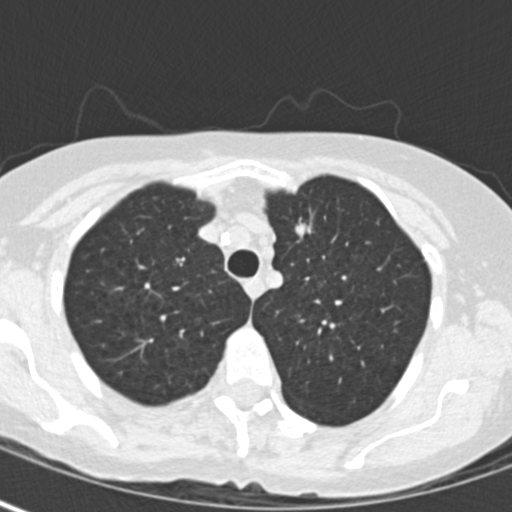
Low-dose screening chest CT, one axial slice. Slice 124 of 163 in the series (ordered by position). Lung window (W 1500 / L -600 HU). 2 mm slice thickness. 512 × 512 image matrix, field of view 280 × 280 mm.
Annotated regions visible in this slice (expert manual segmentation):
- lesion 1 (tumor, upper lobe of left lung): bounding box [x1, y1, x2, y2] px = [295, 217, 312, 242]